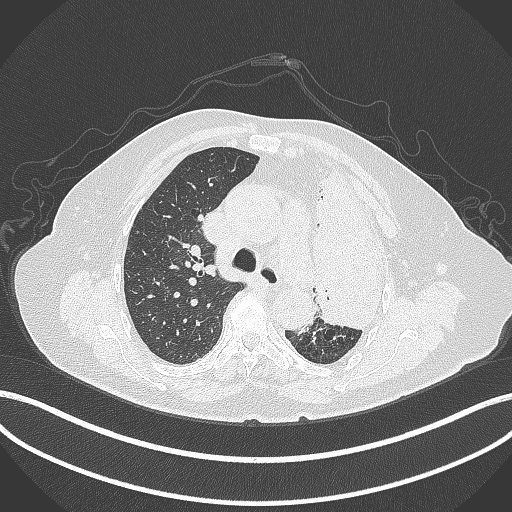
Chest CT, one axial slice. Position 269 of 399 along the scan axis. 120 kVp. Lung window (W 1500 / L -600 HU). 512 × 512 image matrix, field of view 400 × 400 mm. Patient: female, 75 years. Case-level facts recorded for this patient, not image findings: clinical TNM (as recorded): T3 N3 M1.
Annotated regions visible in this slice (rectangle marked by the reading radiologist):
- lung tumour (recorded histology: adenocarcinoma): box from (x=308, y=160) to (x=393, y=332) px